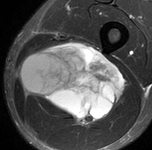
MRI of an extremity soft-tissue mass, one axial slice. Slice 52 of 90 in the series (ordered by position). STIR. MR volume resampled by the dataset authors to the PET/CT grid (not the native acquisition matrix). 3.27 mm slice thickness. 152 × 150 image matrix. Male patient. From the clinical record (not read from this slice): histological type: undifferentiated pleomorphic liposarcoma; grade: high; site of the primary tumour: left thigh.
Outlined on this slice (expert contour drawn on MRI and transferred to this co-registered scan by the dataset authors):
- gross tumour volume including surrounding oedema: bounding box [x1, y1, x2, y2] px = [18, 41, 126, 127]
- gross tumour volume (mass): [20, 41, 126, 127]